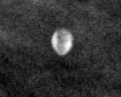
Cropped region of a digitized screen-film mammogram centred on a radiologist-marked abnormality; right breast; CC view; BI-RADS breast density category 1 (scale 1–4).
Marked abnormality: calcifications, morphology lucent center; BI-RADS assessment category 2; benign without callback (not worked up further).